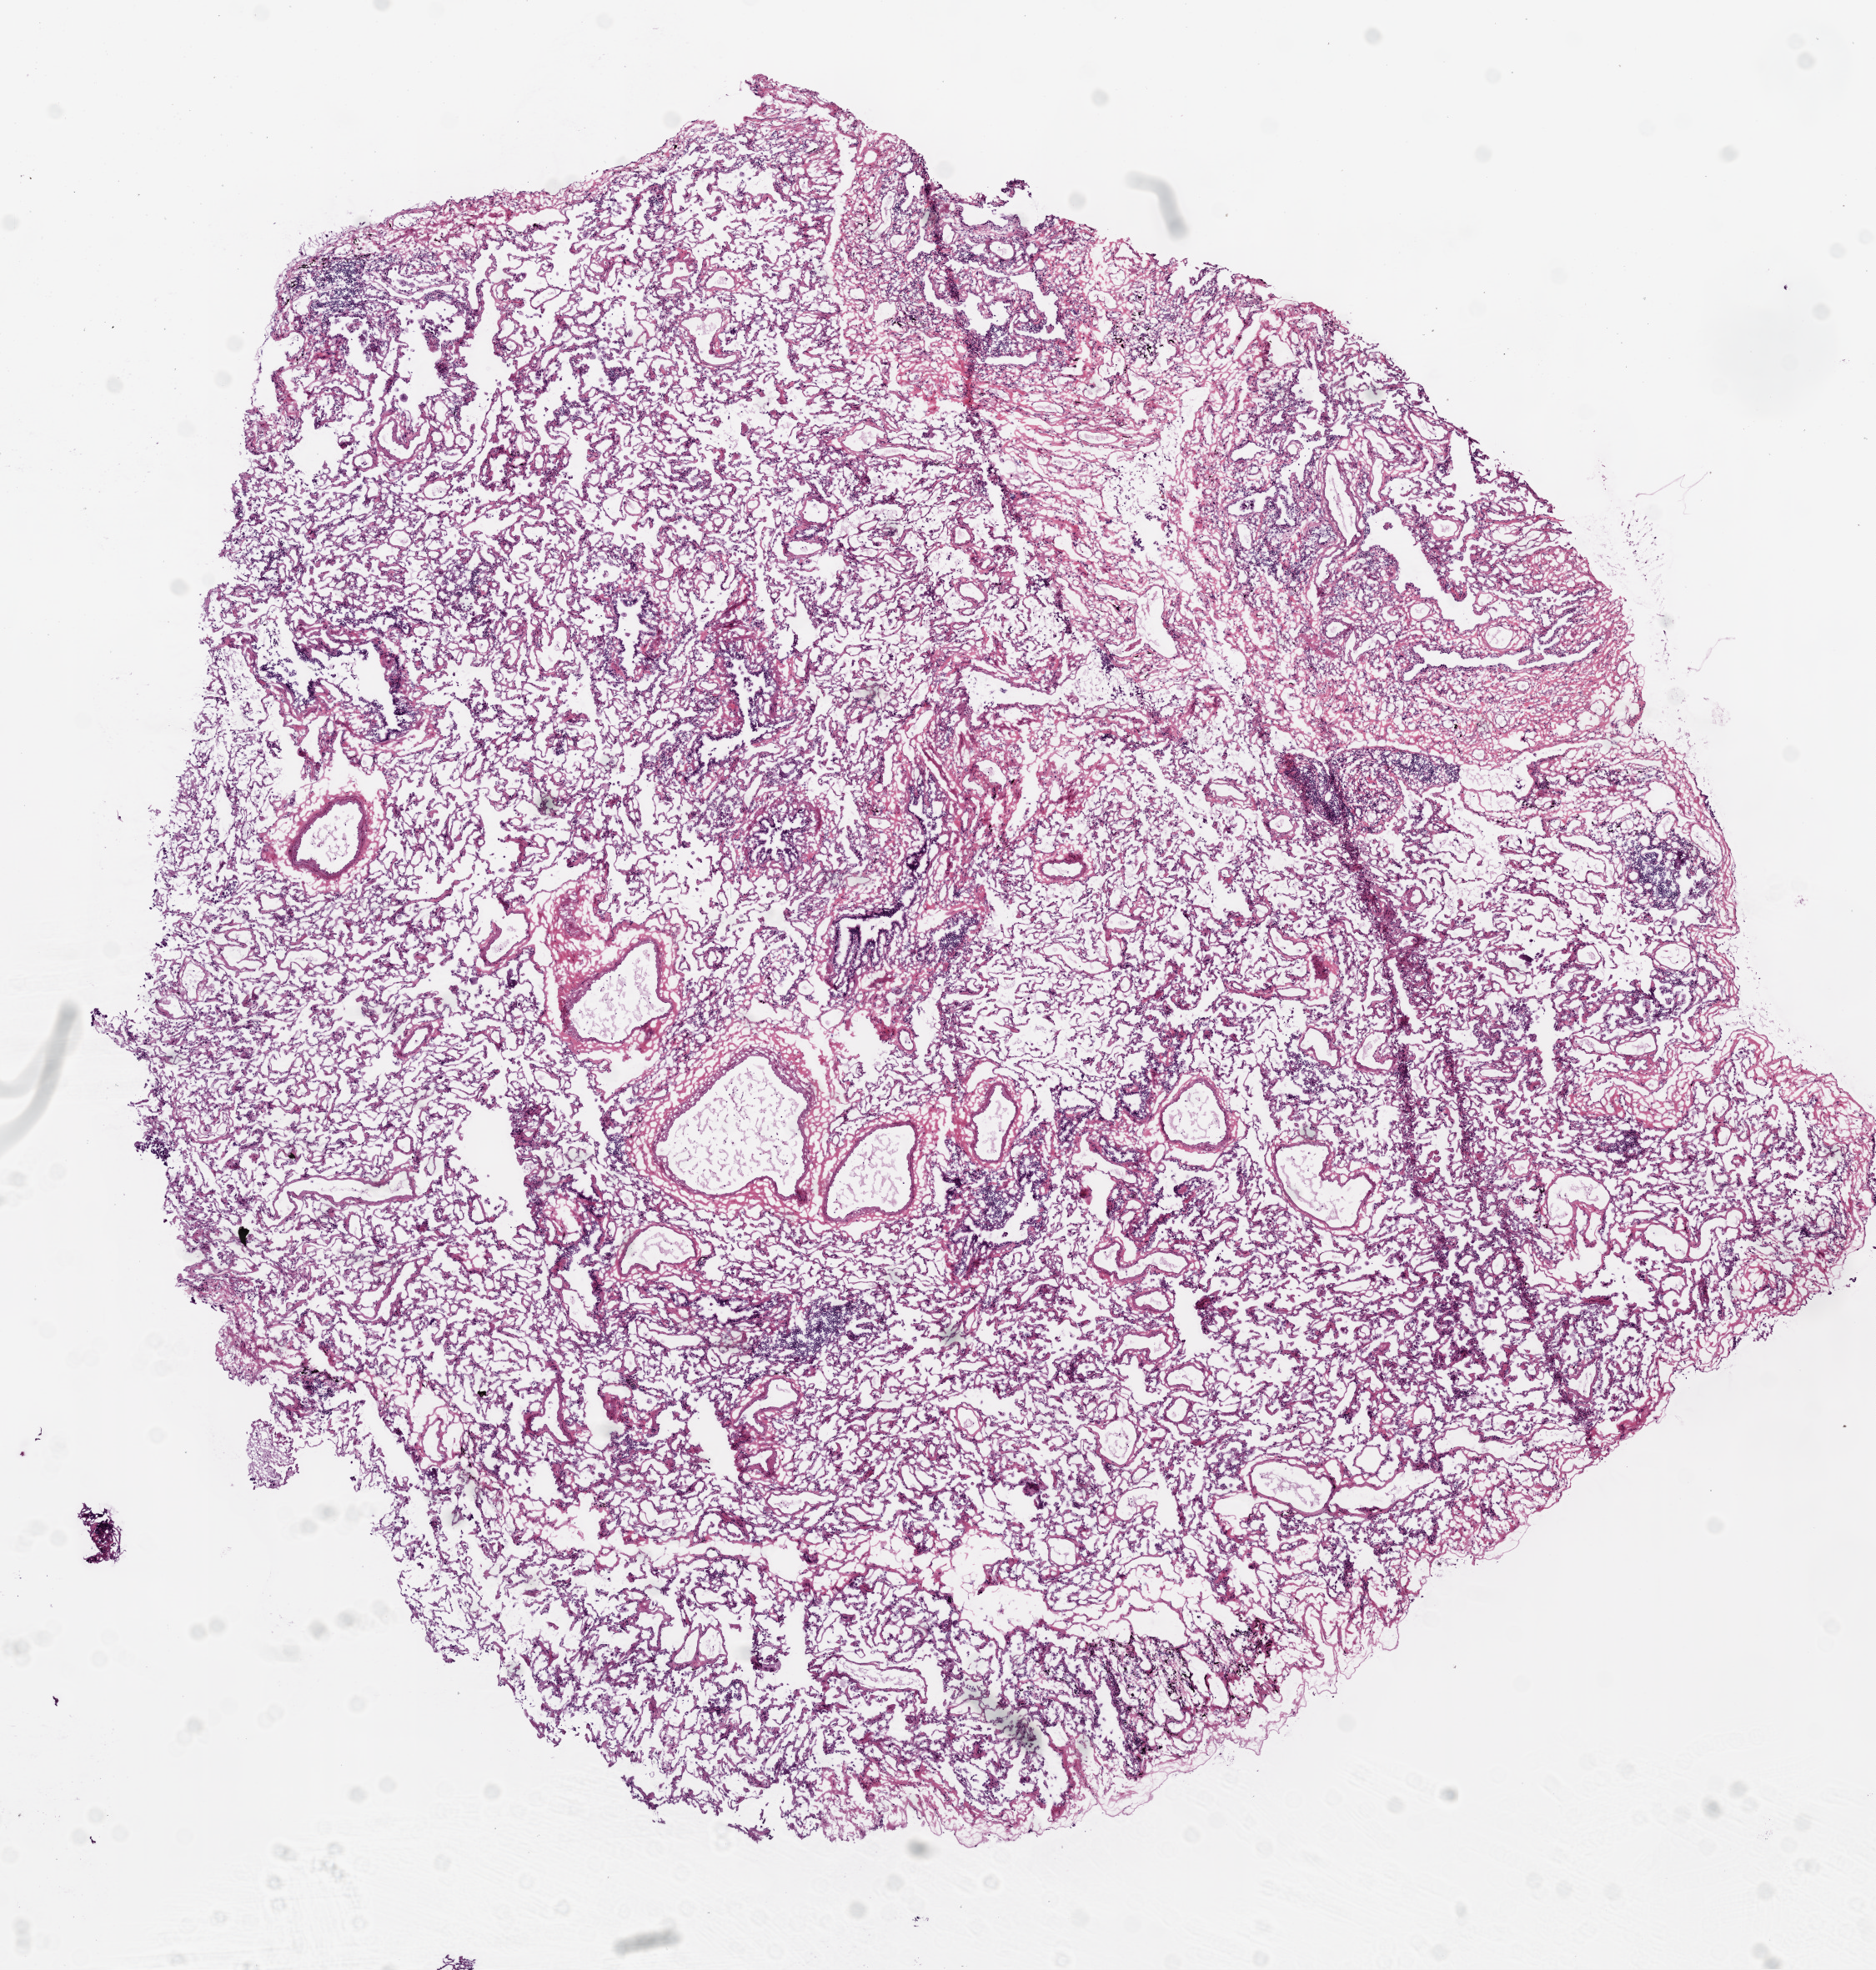
Hematoxylin and eosin (H&E) stained whole-slide image — shown as a low-resolution overview of the whole scanned area (about 9.0 x 9.5 mm). Frozen section from the bottom of the tissue portion. Sample: solid tissue normal (non-tumour tissue), lung. Female, age 74 years at initial diagnosis.
This section: solid tissue normal sample (biorepository sample class). Patient diagnosis: Adenocarcinoma, NOS (lower lobe, lung).